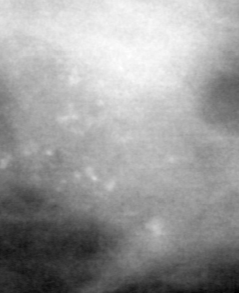
Cropped region of a digitized screen-film mammogram centred on a radiologist-marked abnormality, right breast, CC view.
Calcifications, morphology pleomorphic, distribution clustered; BI-RADS assessment category 4; pathology (as recorded): malignant.